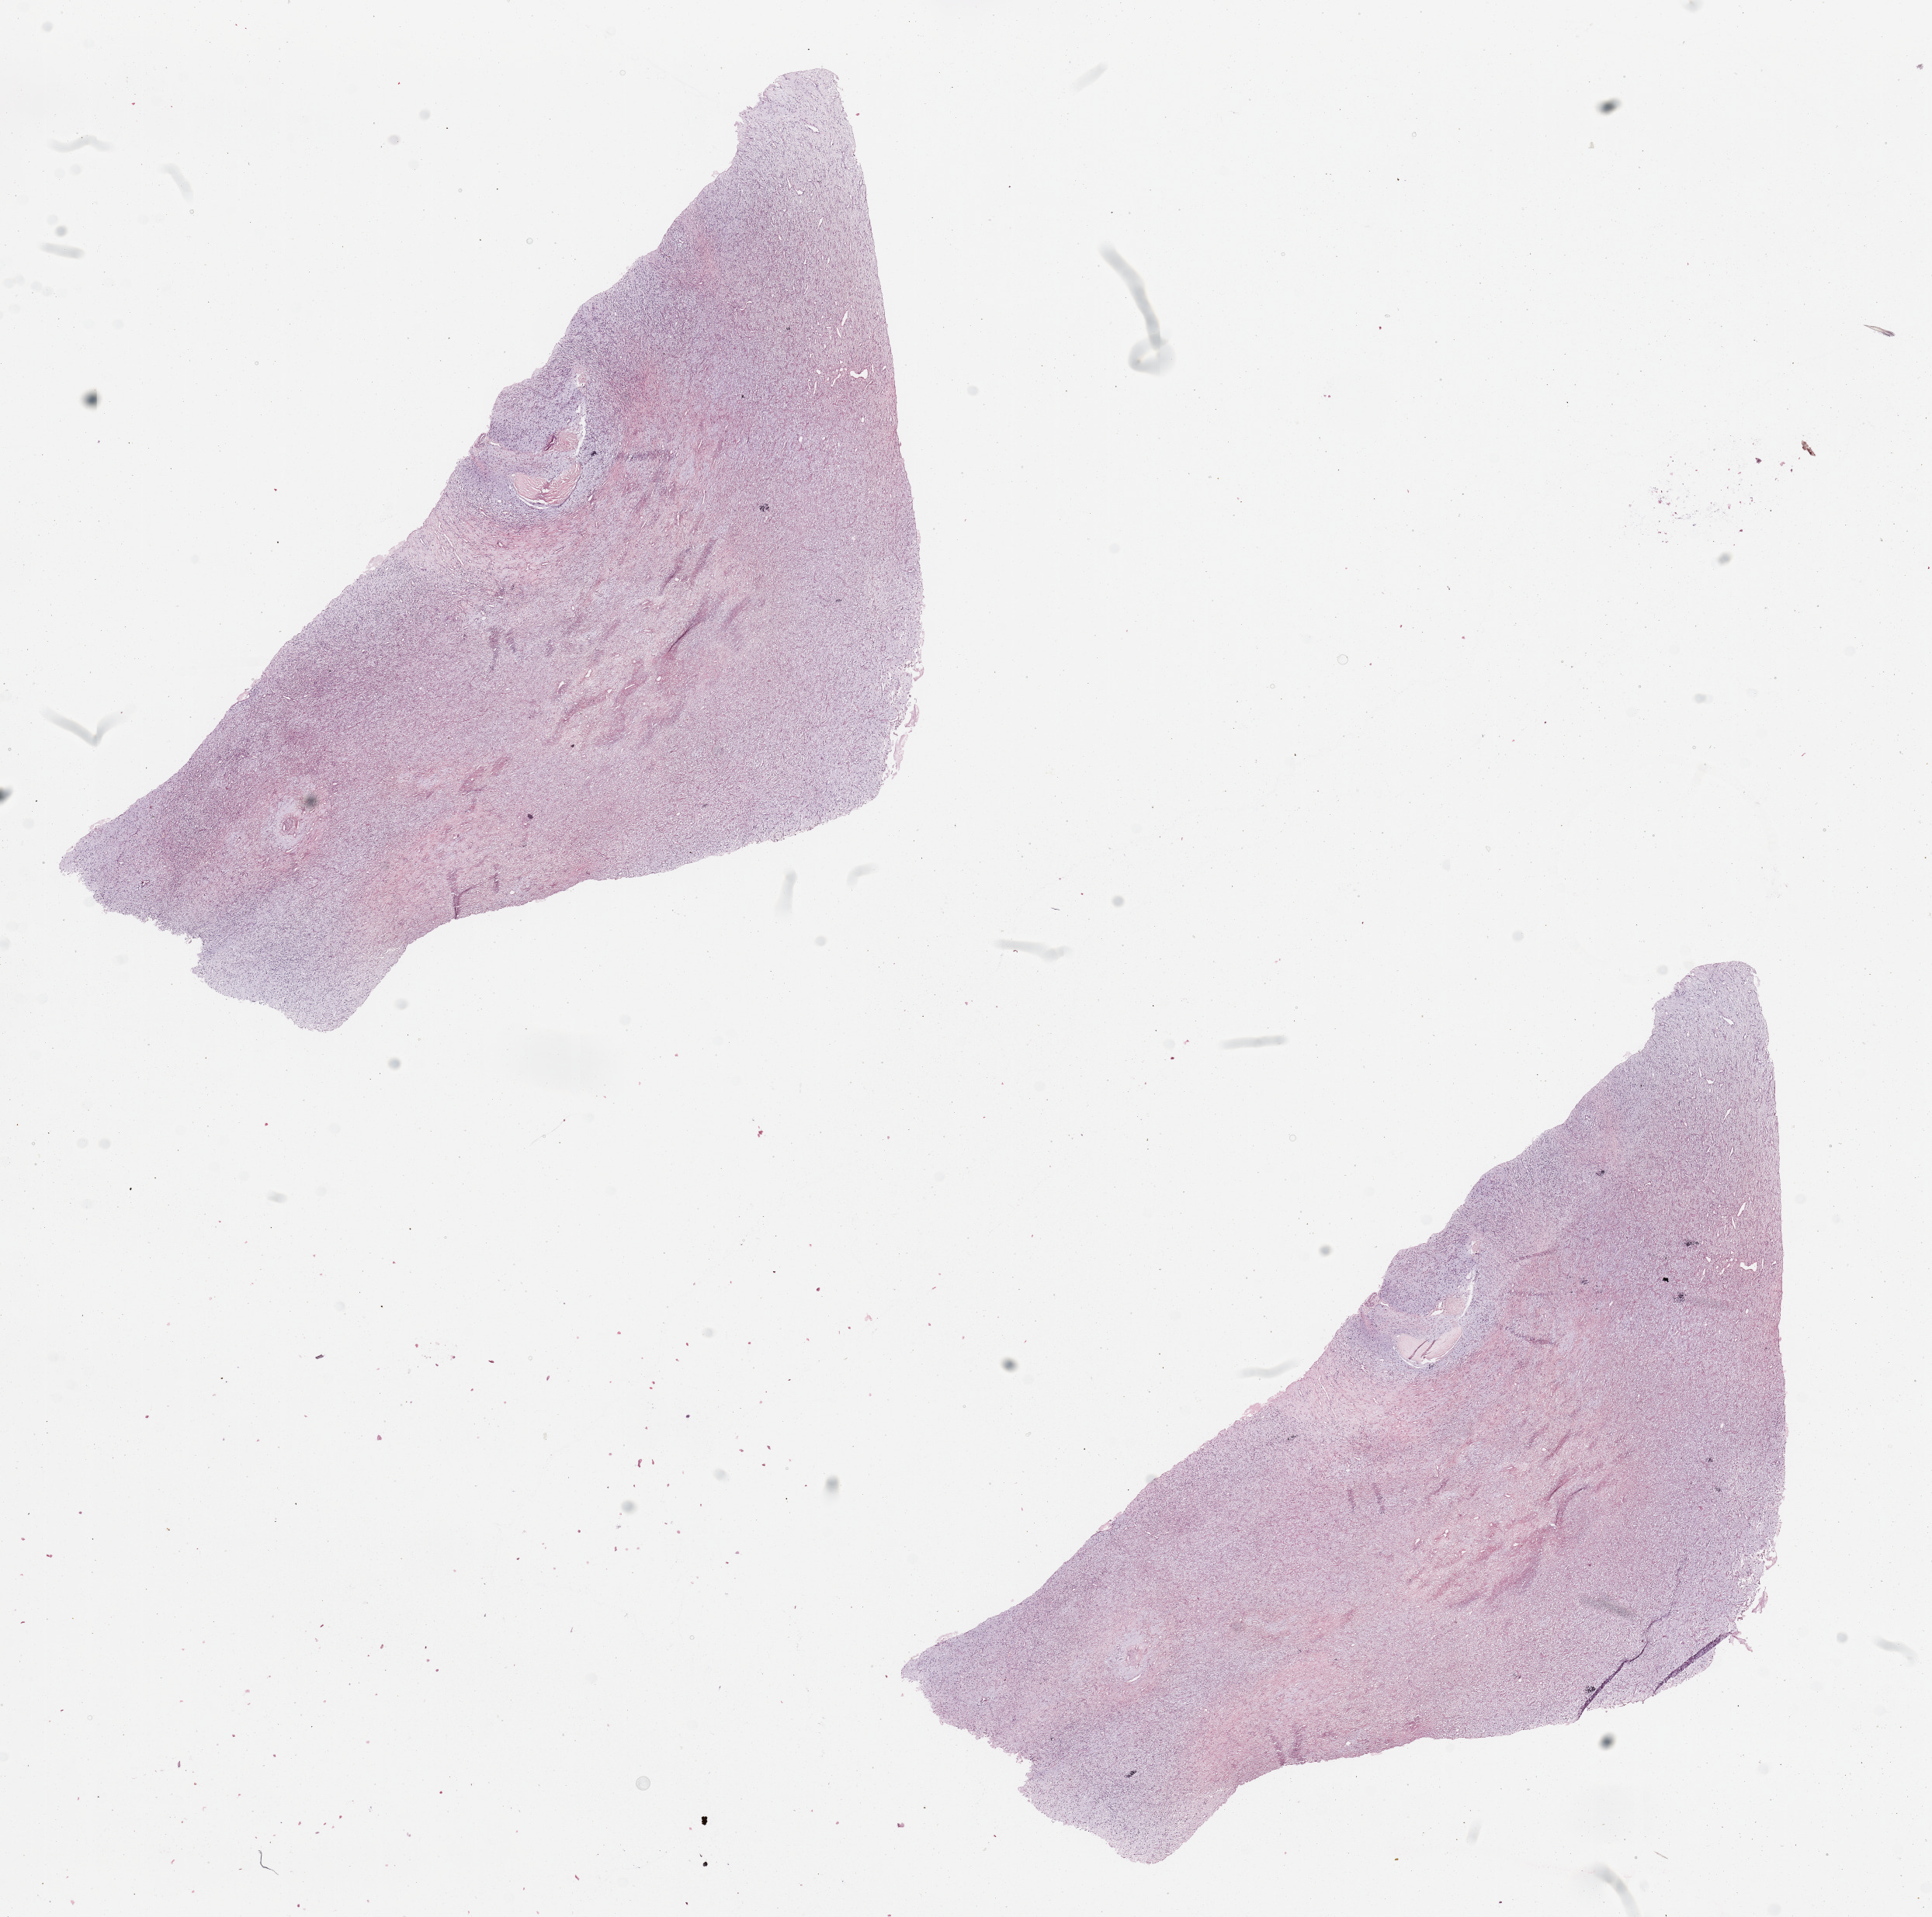
Whole-slide histology image, H&E — shown as a low-resolution overview of the whole scanned area (about 19.7 x 19.5 mm, acquisition: 20x scan). Tumour tissue sample. Patient: male, age 42 years.
Patient diagnosis (cohort enrolment): sarcoma (site not recorded at cohort level). Primary tumour site (as recorded): lower extremity.